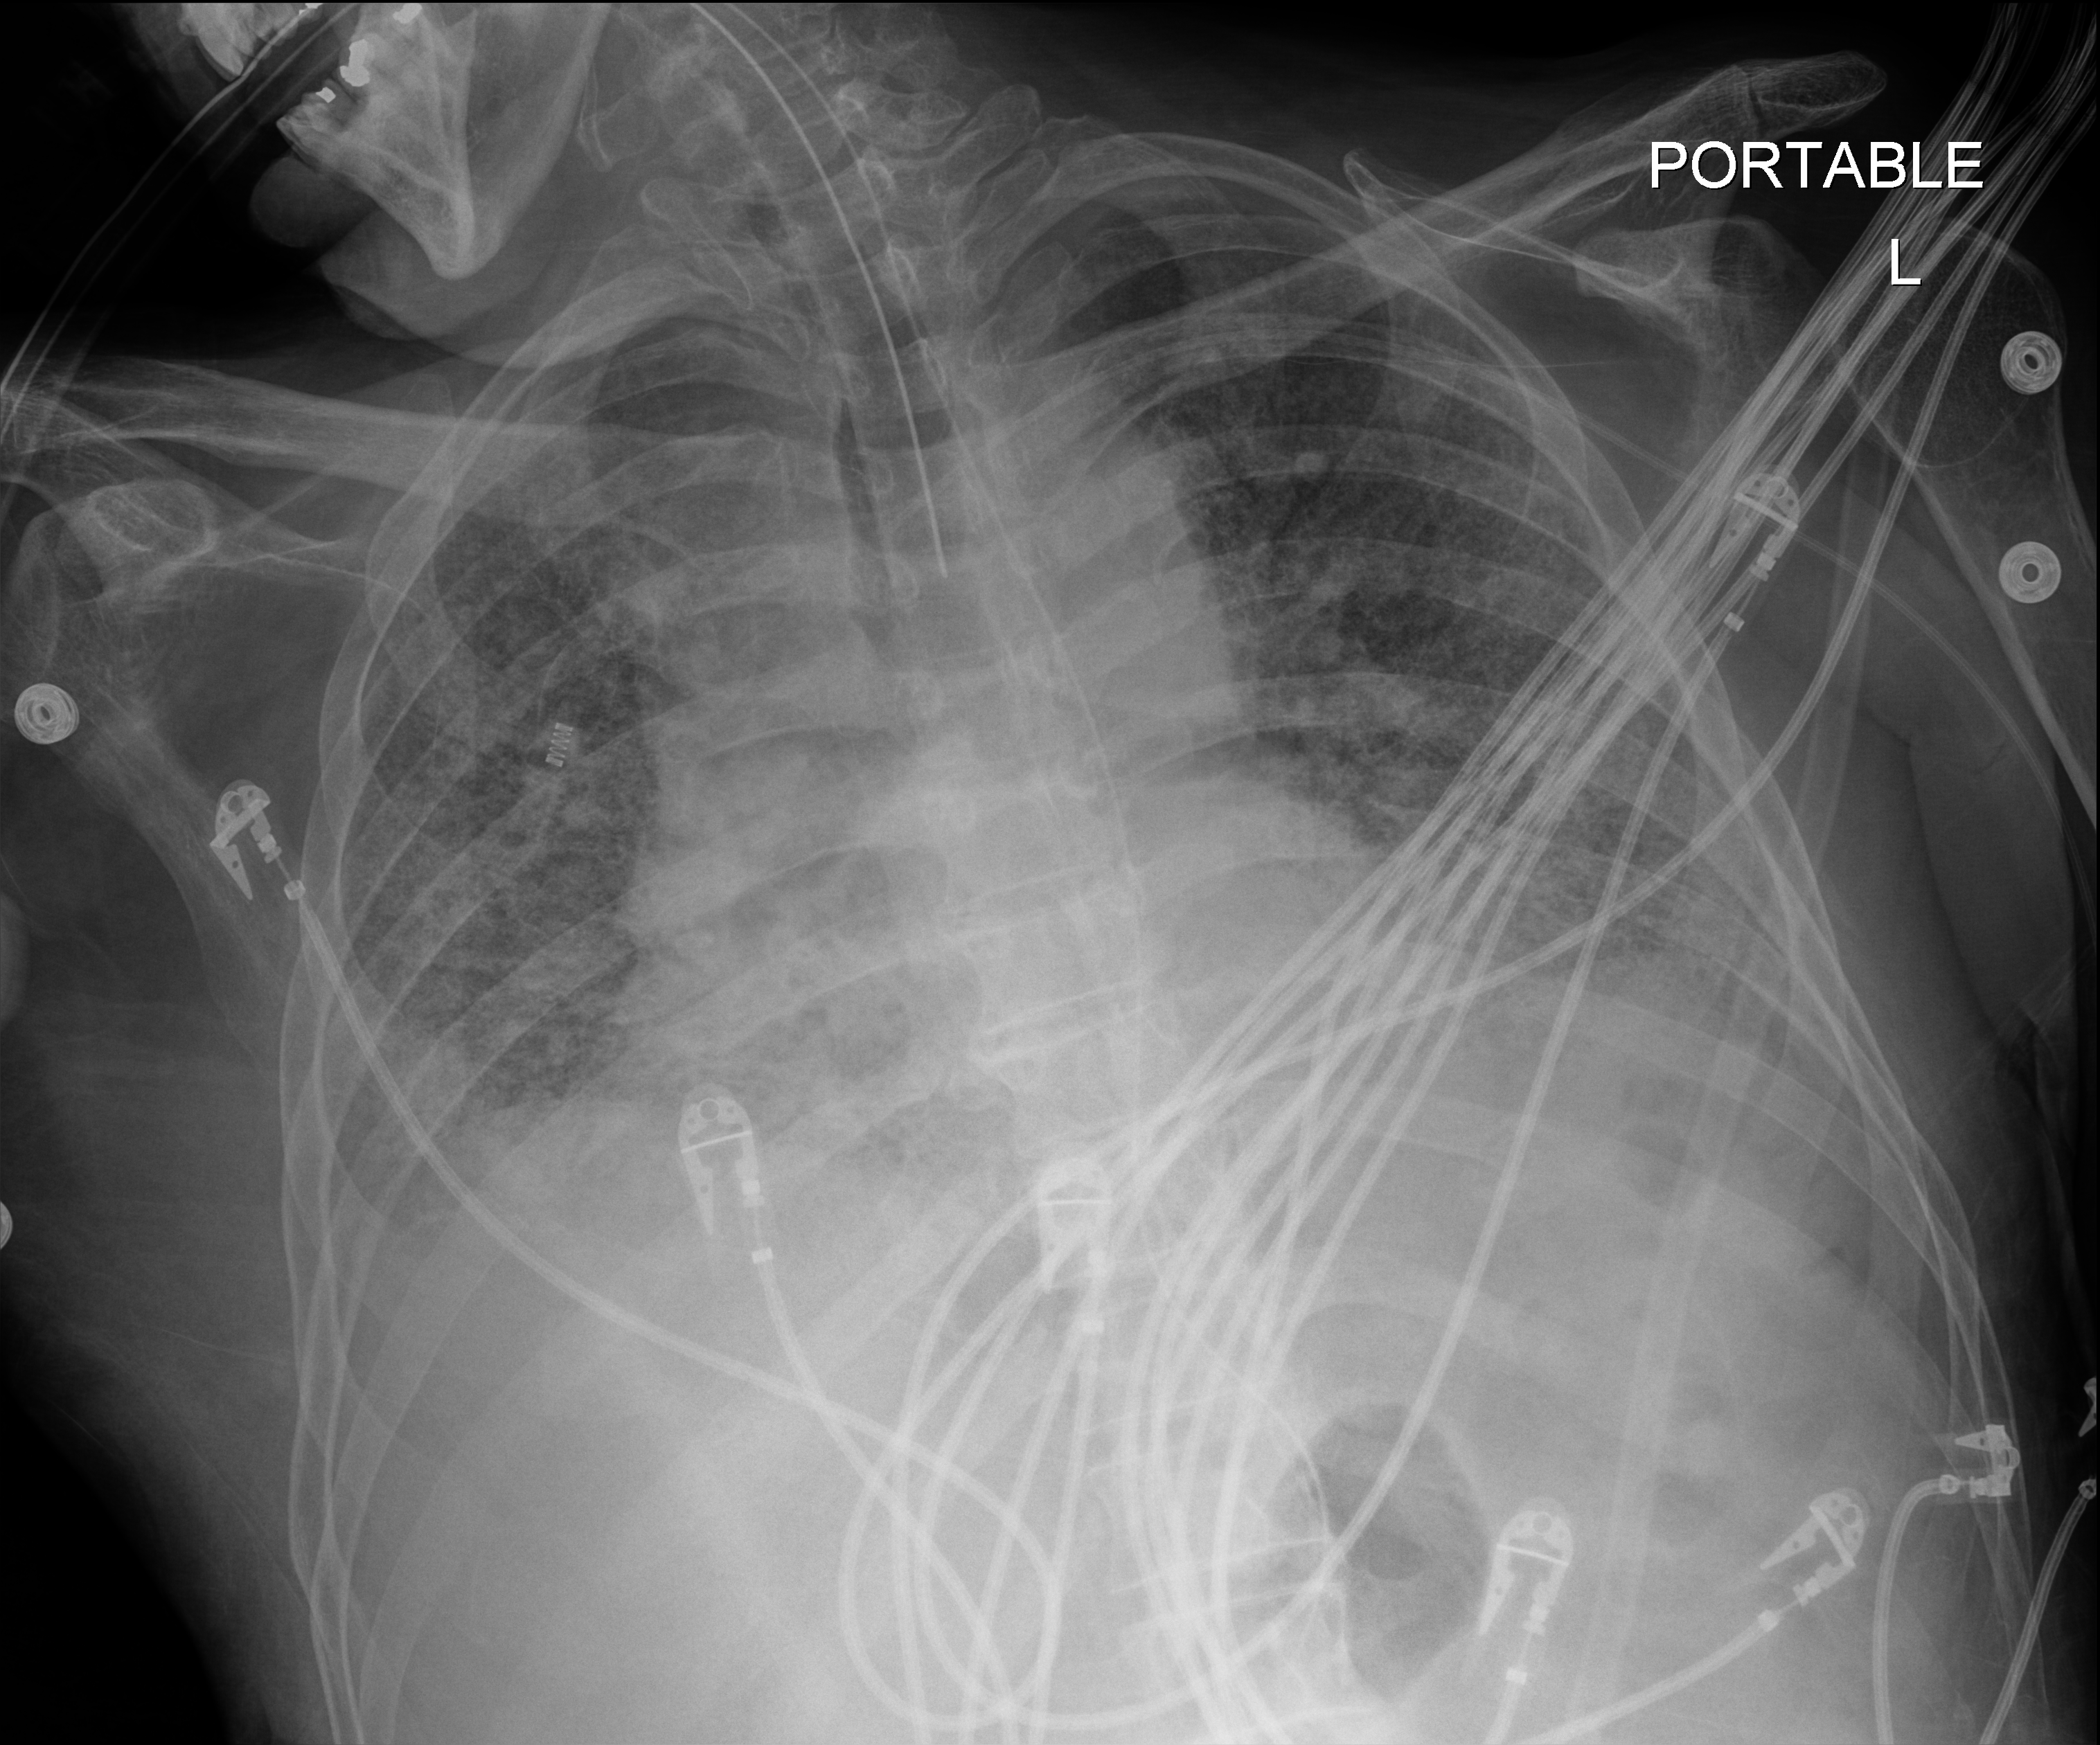
Chest radiograph (digital radiography), anteroposterior (AP) projection. Patient hospitalised with COVID-19; male, aged 60–74 years.
From the hospital-stay record, not from the radiograph (when in the stay this image was taken is not recorded): mechanically ventilated during this hospital stay: yes; admitted to intensive care during this hospital stay: yes.